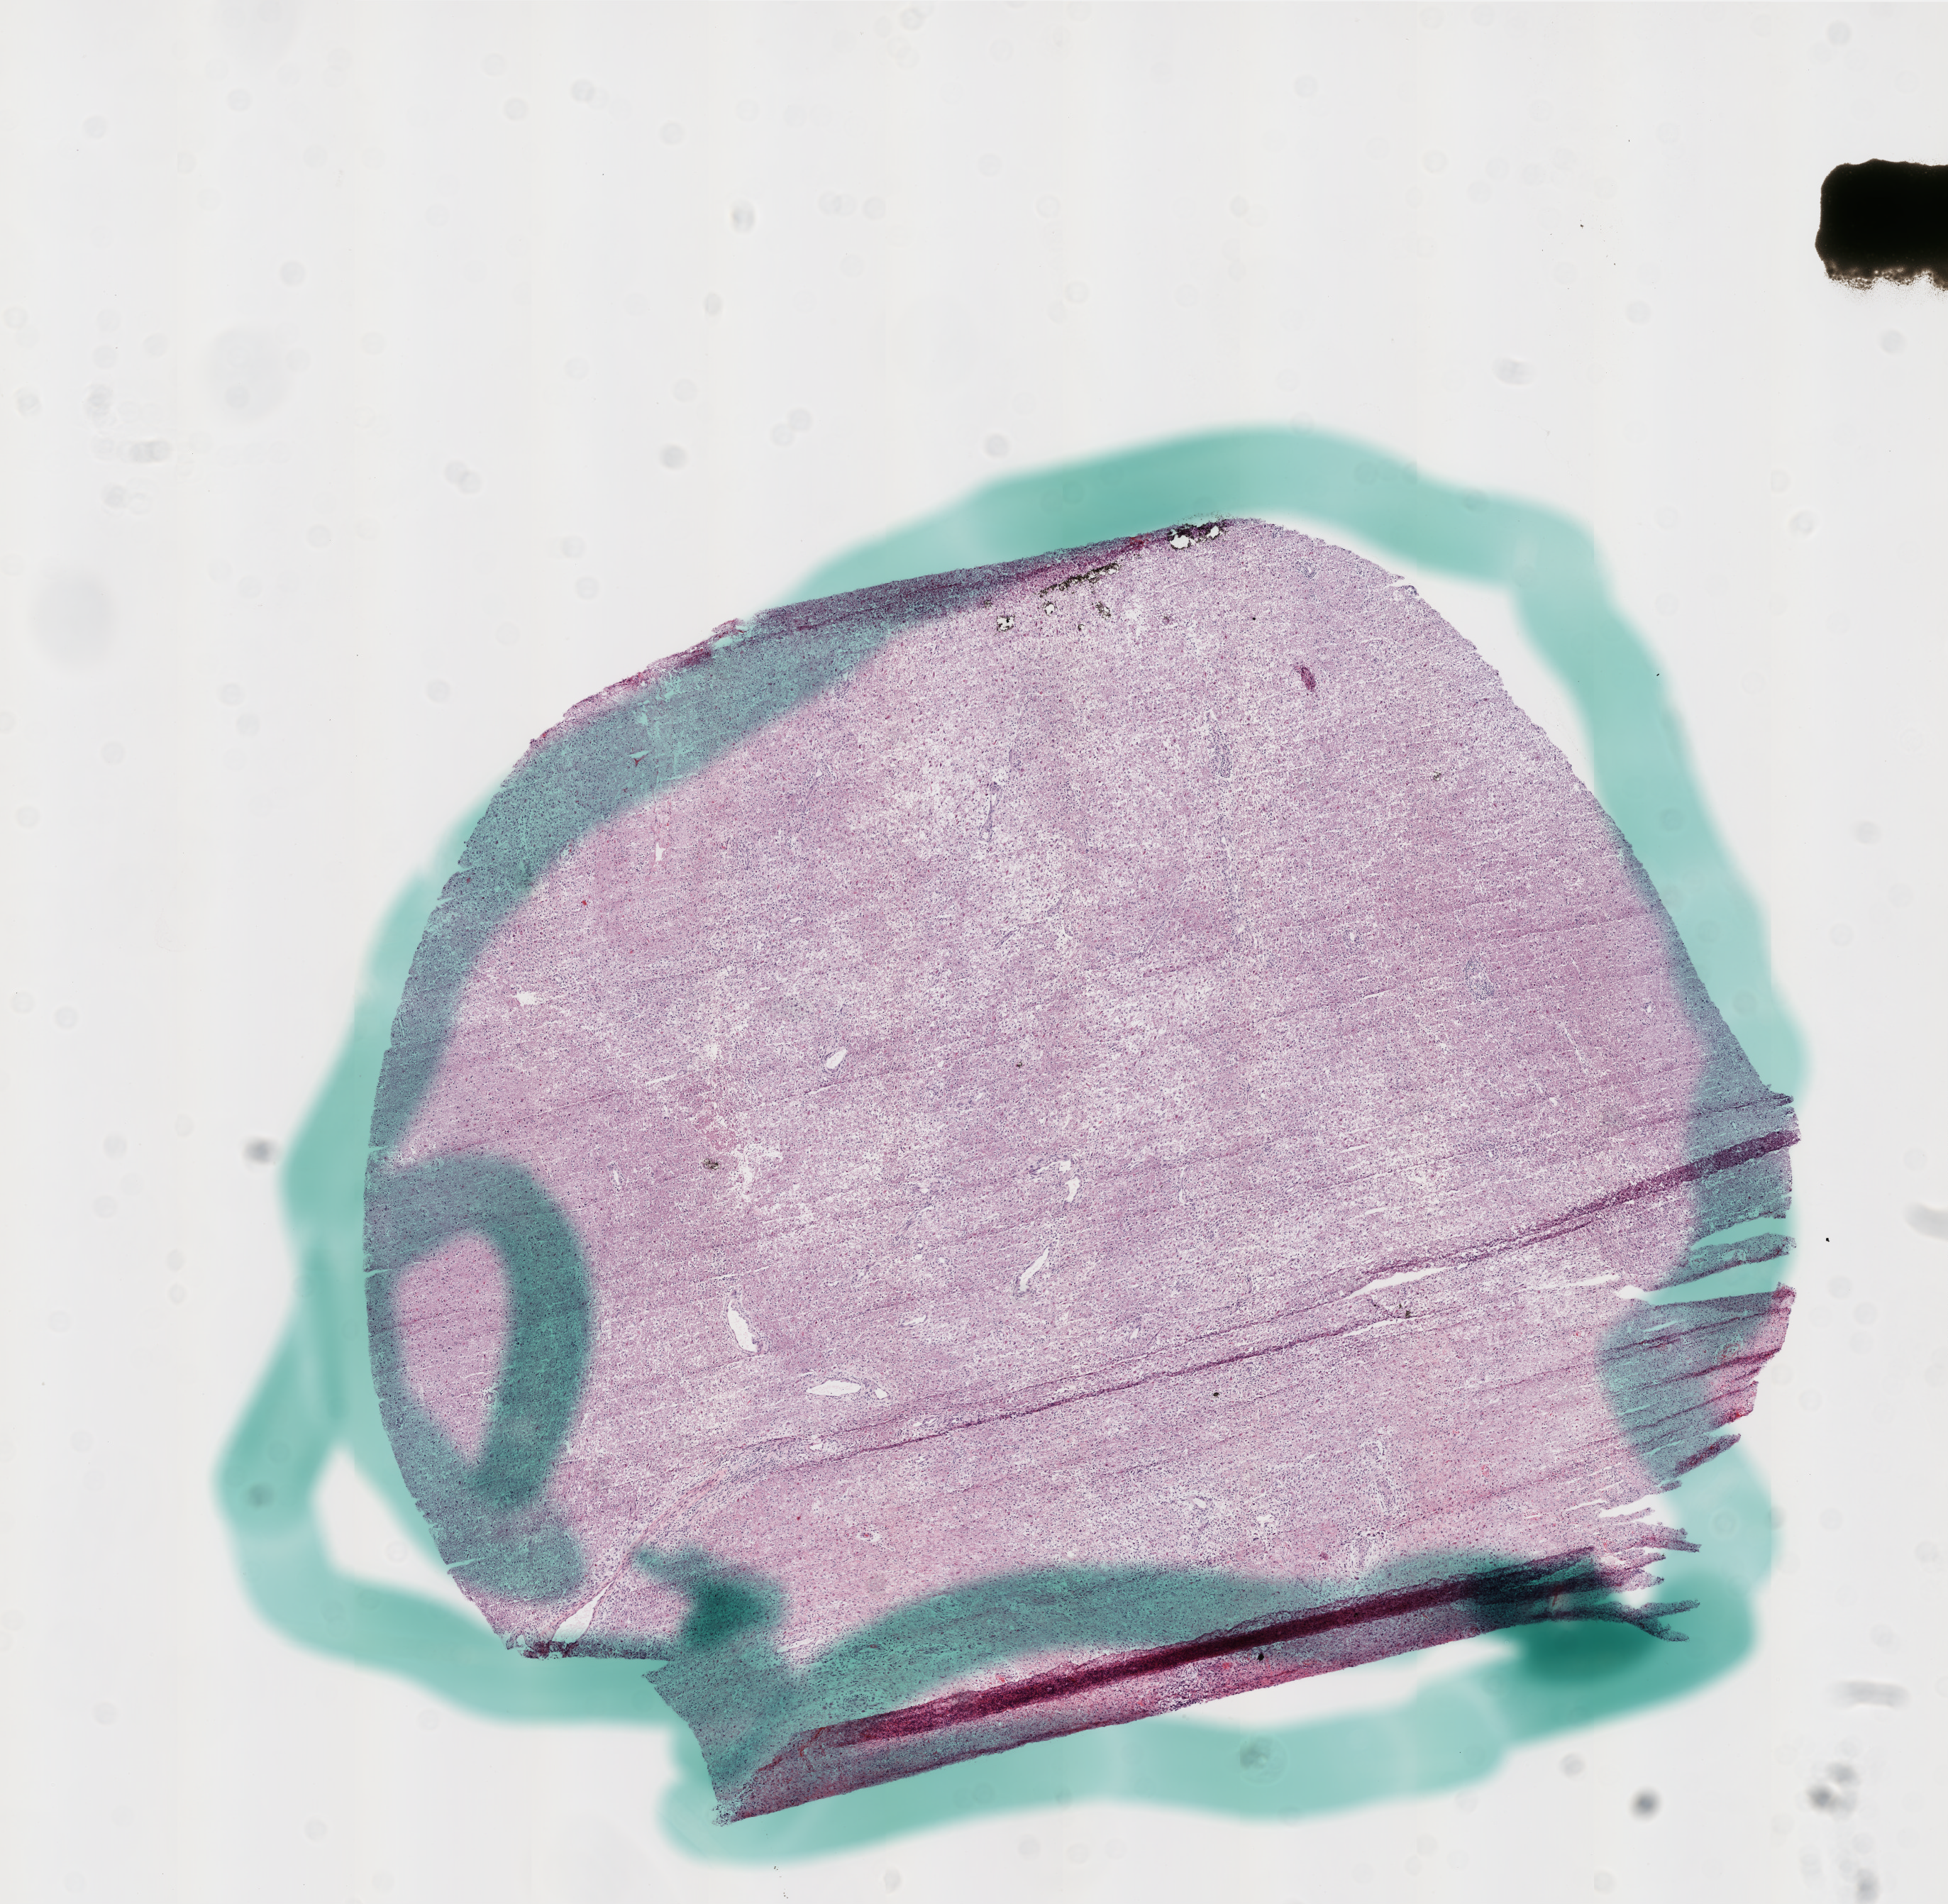
H&E-stained whole-slide image, a low-resolution overview of the entire scanned area, about 11.0 x 10.7 mm (from a 20x scan), frozen section from the bottom of the tissue portion, primary tumour sample from the brain. Patient: male, age at initial diagnosis 49 years. Slide review estimates, as recorded: tumour cells 90%, tumour nuclei 100%, normal cells 10%, stromal cells 0%, necrosis 0%.
- pathologic diagnosis: Glioblastoma